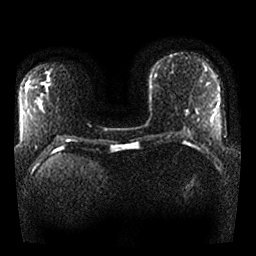
Breast MRI, one axial slice. Position 11 of 25 along the scan axis. Diffusion-weighted series; image 2 of 4 stored at this slice position (different b-values; order by instance number). 1.5 T. 256 × 256 image matrix. Female patient.
Structures marked on this image (expert manual segmentation):
- tumour on diffusion-weighted imaging: bounding box <45,78,50,86> (left, top, right, bottom; pixels)